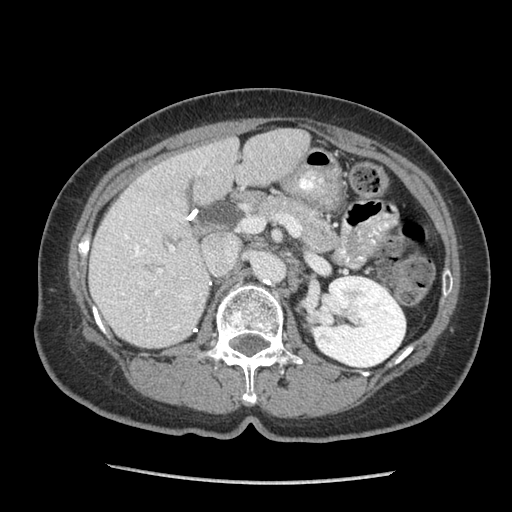
Contrast-enhanced abdominal CT (liver protocol), one axial slice; slice 40 of 105 in the series (ordered by position); 140 kVp; soft-tissue window (W 400 / L 40 HU); 2.5 mm slice thickness; 512 × 512 image matrix. Case-level facts recorded for this patient, not image findings: diagnosis: hepatocellular carcinoma (patient treated with transarterial chemoembolisation; whether this scan precedes or follows treatment is not stated here); TNM stage (as recorded): Stage-I; Child-Pugh class: A.
Annotated regions visible in this slice (semi-automatic segmentation, software-assisted and operator-edited):
- liver parenchyma outside the tumour (the mass and vessels are separate outlines, so this box may not span the whole liver): bounding box <88,128,310,348> (left, top, right, bottom; pixels)
- liver vessels: <106,153,202,330>